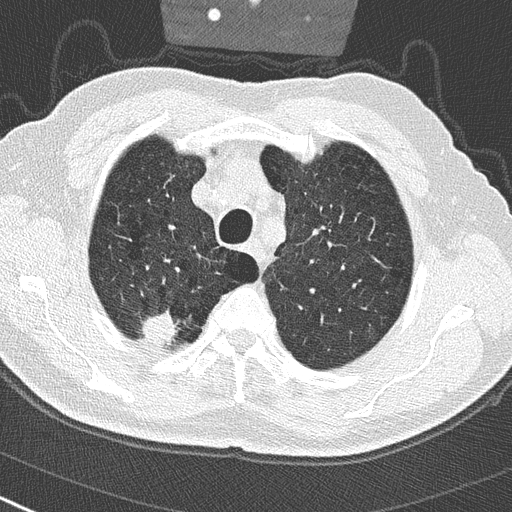
Low-dose screening chest CT, one axial slice; reconstruction kernel B50f; 120 kVp; lung window (W 1500 / L -600 HU); 512 × 512 image matrix, field of view 300 × 300 mm.
Annotated regions visible in this slice (manually delineated by an expert):
- lesion 1 (tumor, upper lobe of right lung): bounding box <141,313,176,345> (left, top, right, bottom; pixels)